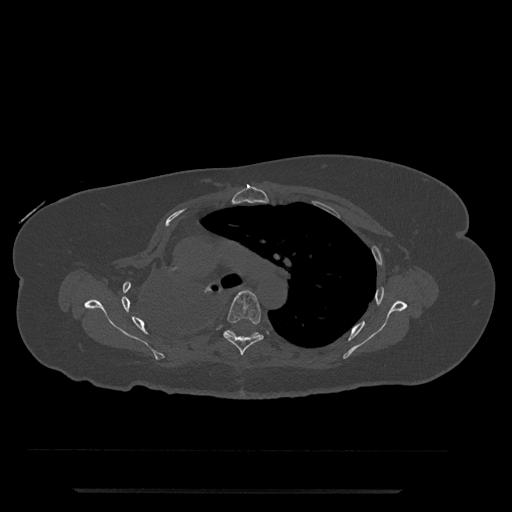
CT including the spine, one axial slice. Slice 537 of 797 in the series (ordered by position). 120 kVp. Bone window (W 1800 / L 400 HU). 512 × 512 image matrix. Female patient, age 51 years. Case-level facts recorded for this patient, not image findings: primary cancer: neuro.
Structures marked on this image (semi-automatically segmented with operator editing):
- T5 vertebra: box from (x=223, y=290) to (x=264, y=355) px
- T6 vertebra: (x=225, y=330)–(x=259, y=337)